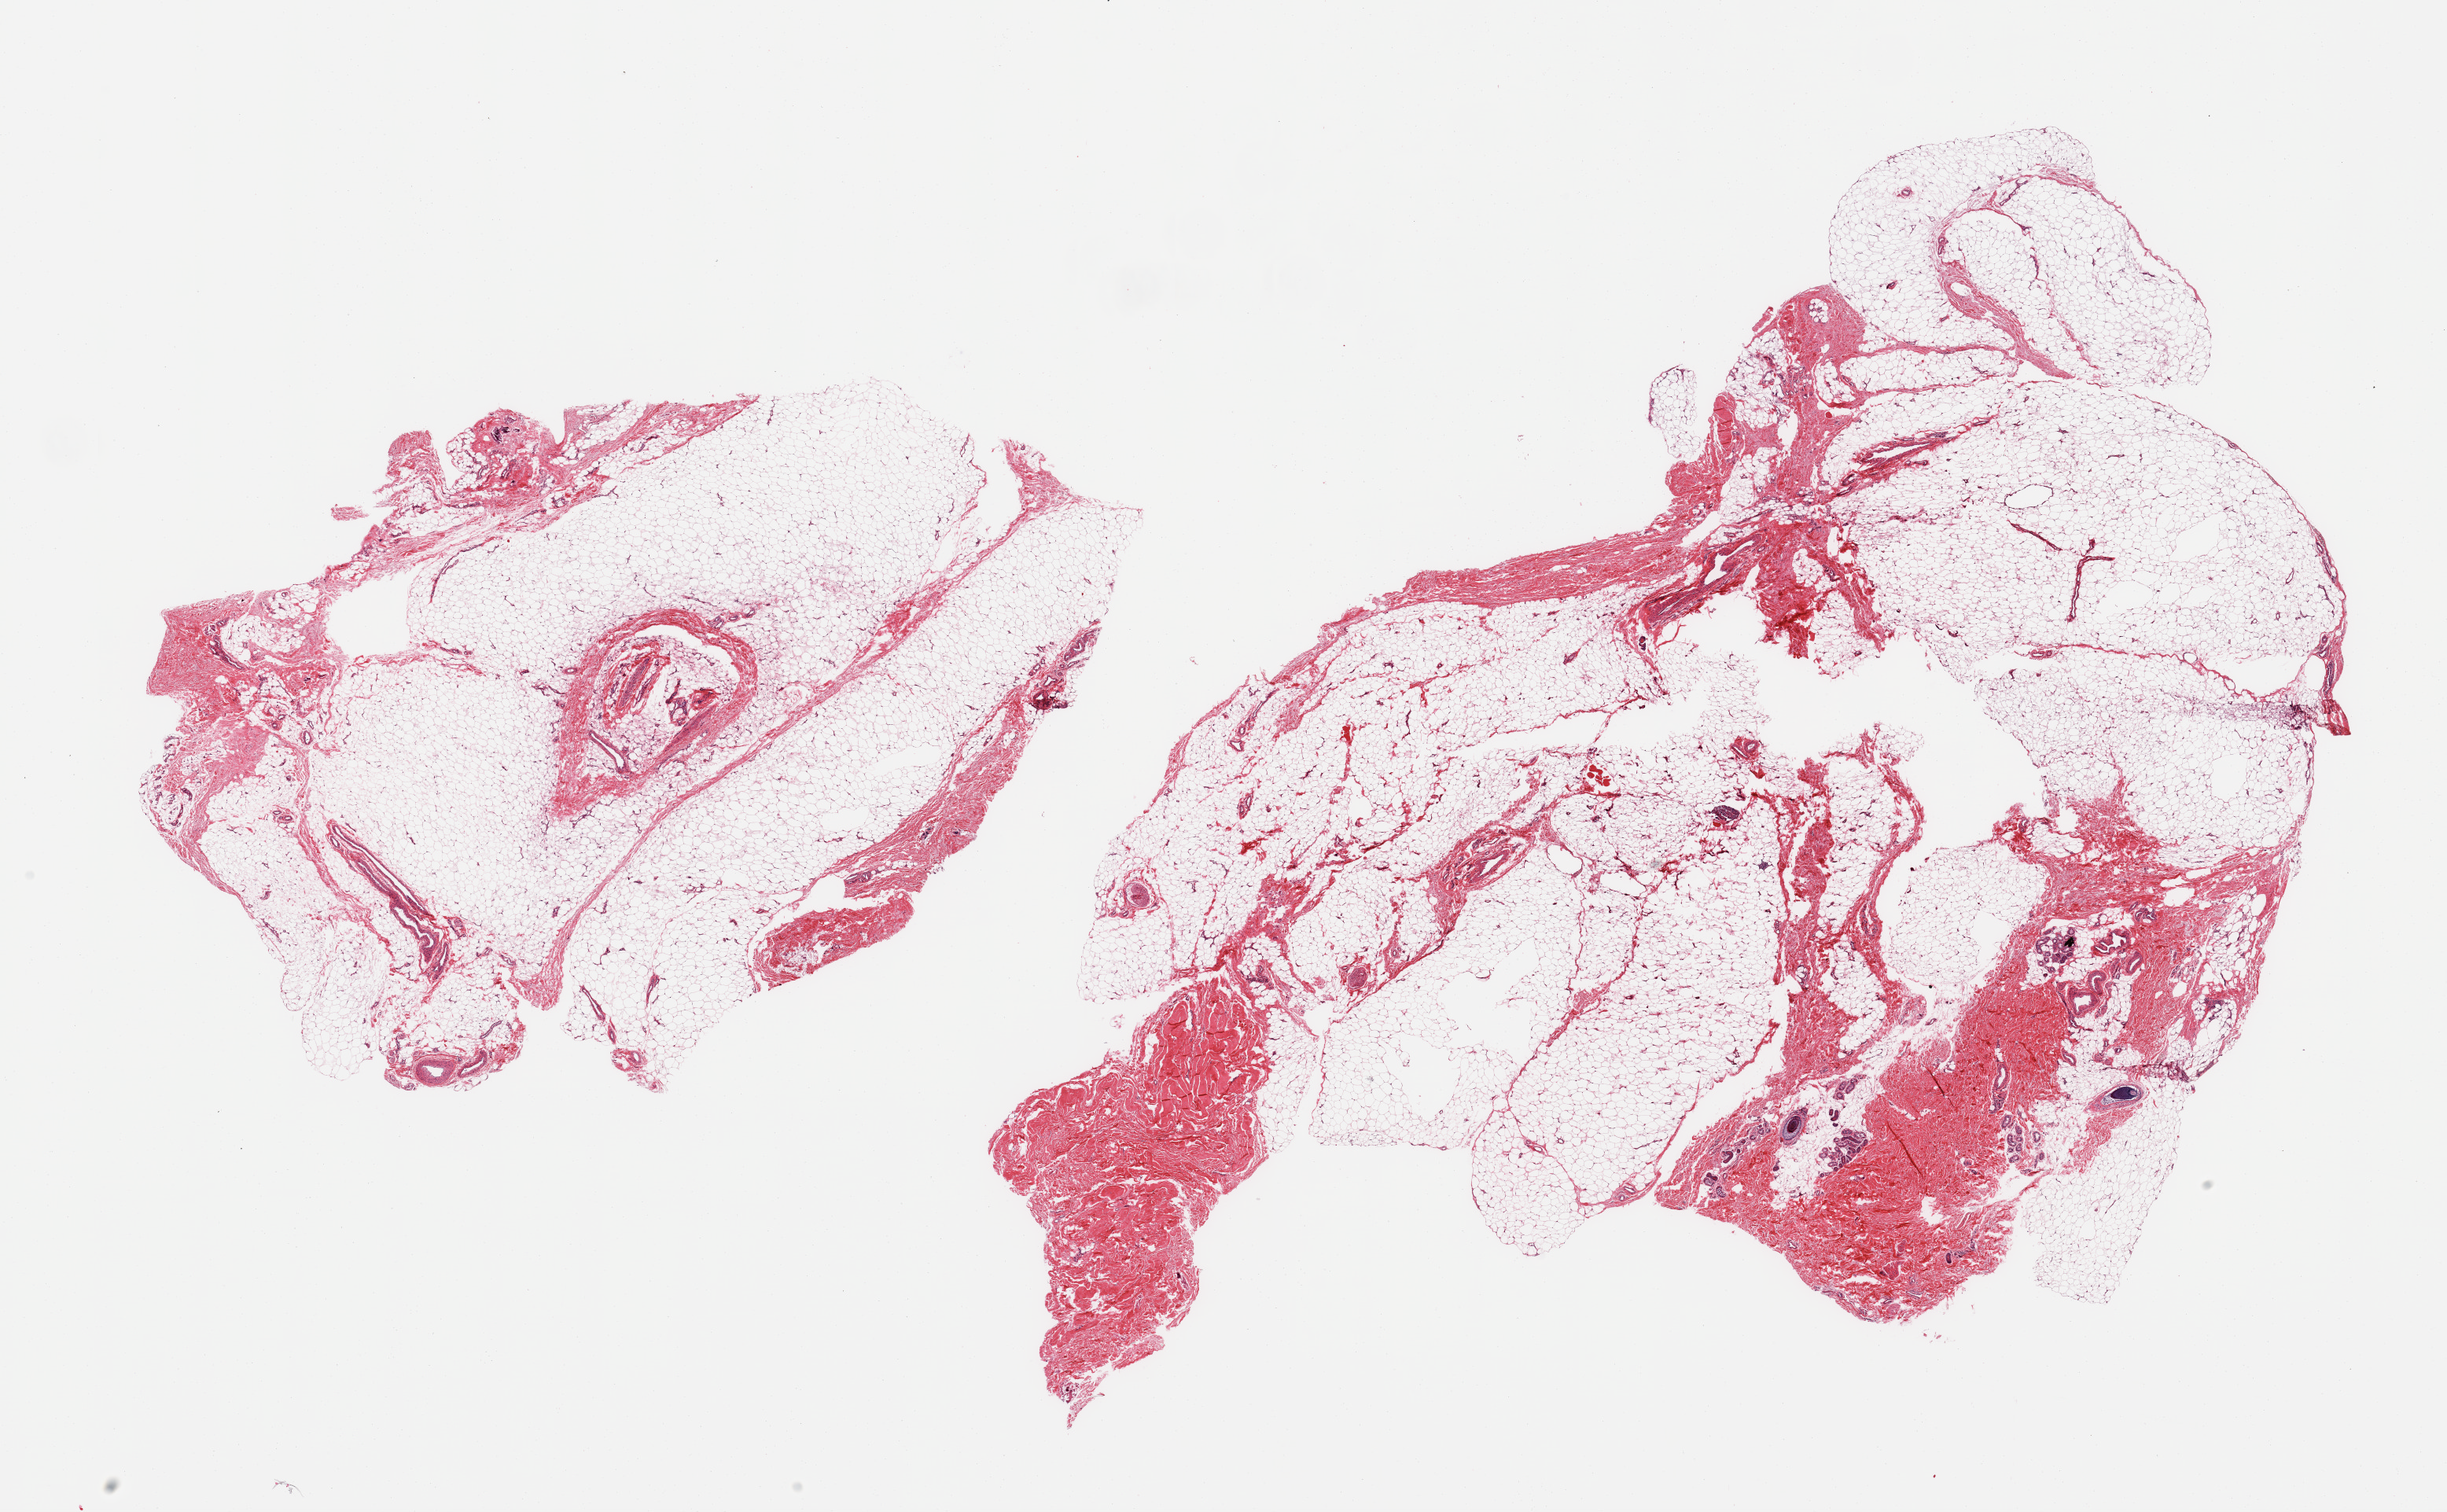
Digitized haematoxylin and eosin-stained section, brightfield — whole scanned area (about 24.6 x 15.2 mm) shown as a low-resolution overview. PAXgene-fixed, paraffin-embedded tissue. Section of adipose tissue (target tissue). Tissue donor sample. Donor: male.
* pathologist's review note for this sample: 2 pieces; from 10-30% is fibrous tissue/tendon, hair follicles/sweat glands, vessels